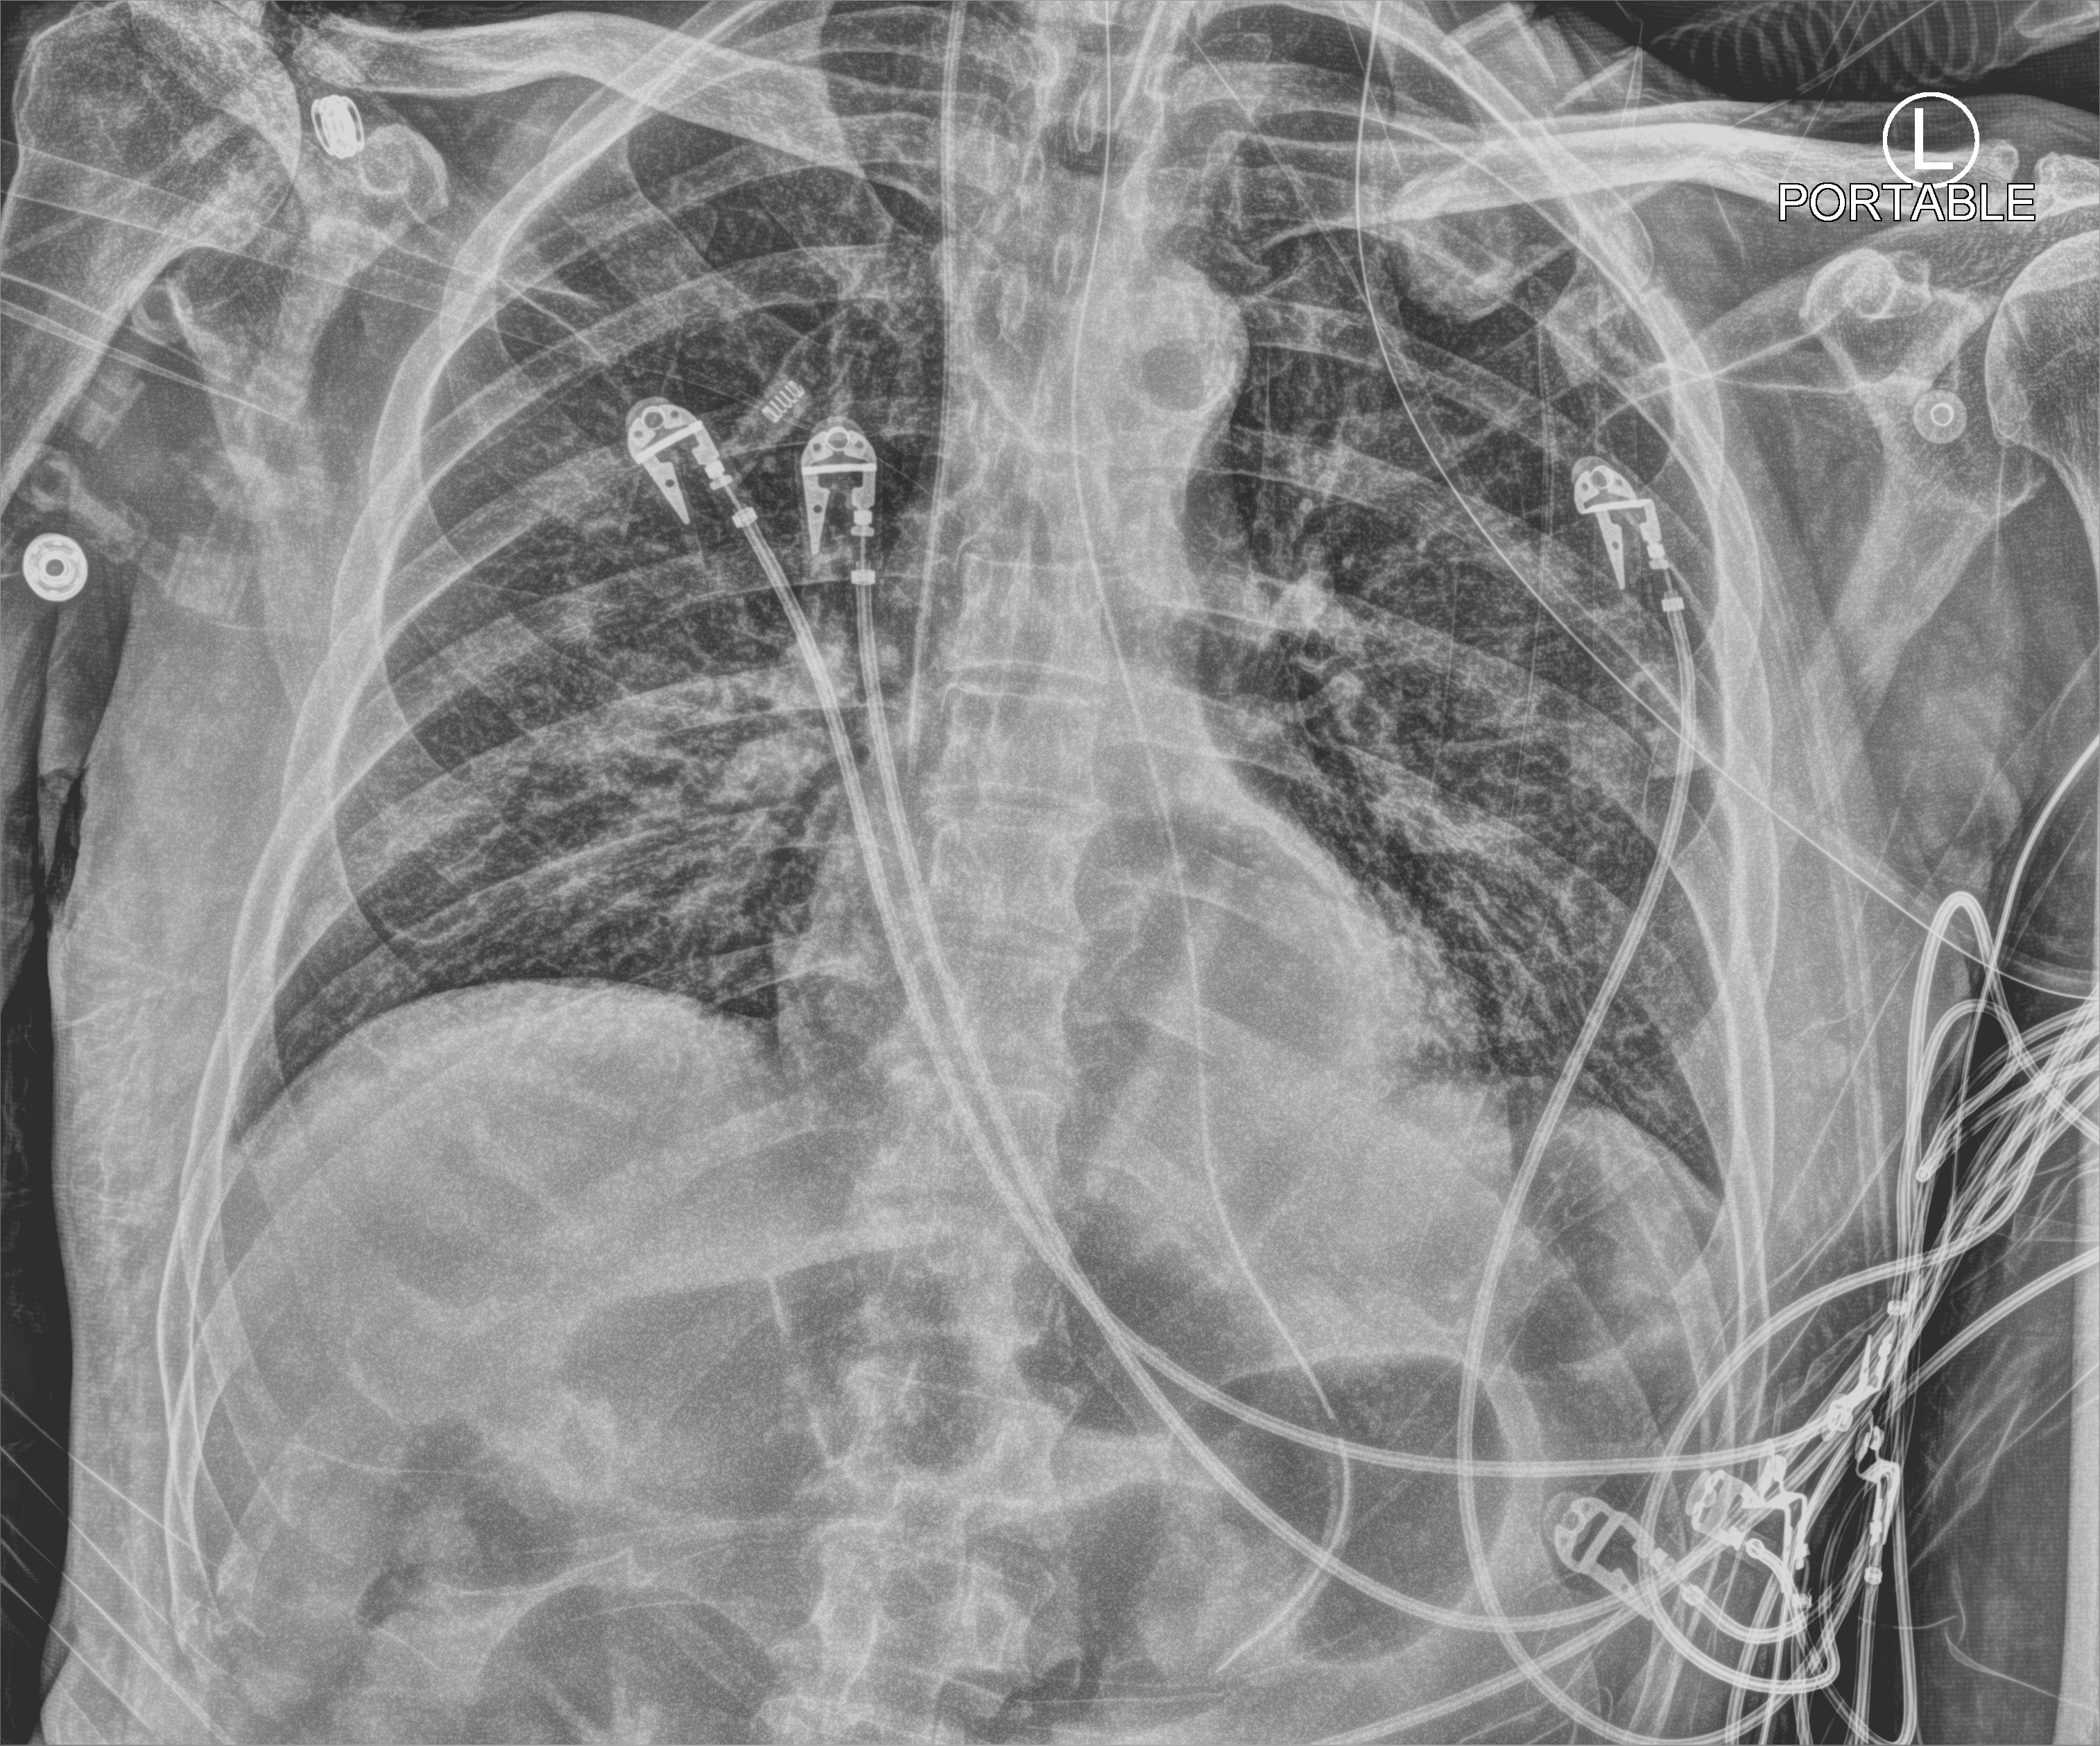
Portable chest radiograph, anteroposterior (AP) projection. Male patient hospitalised with COVID-19, age 75–90 years.
Admission-level facts for this patient (not findings on this image; timing relative to this image not recorded):
- admitted to intensive care during this hospital stay: yes